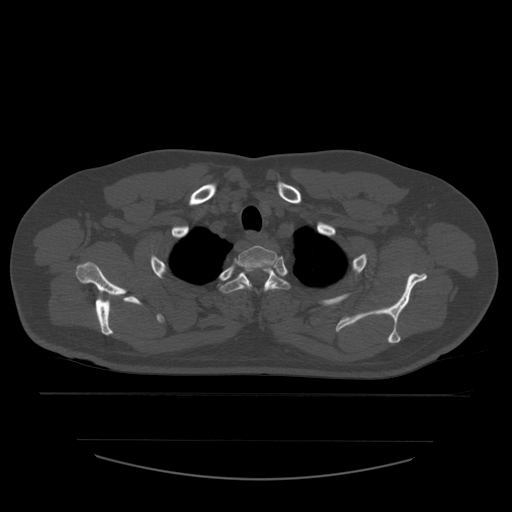
CT including the spine, one axial slice. Position 456 of 532 along the scan axis. Bone window (W 1800 / L 400 HU). 512 × 512 image matrix, field of view 441 × 441 mm. Patient age 44 years. From the clinical record (not read from this slice): primary cancer: soft tissue sarcoma.
Annotated regions visible in this slice (semi-automatic segmentation, software-assisted and operator-edited):
- T1 vertebra: box from (x=237, y=246) to (x=278, y=270) px
- T2 vertebra: (x=220, y=268)–(x=290, y=294)